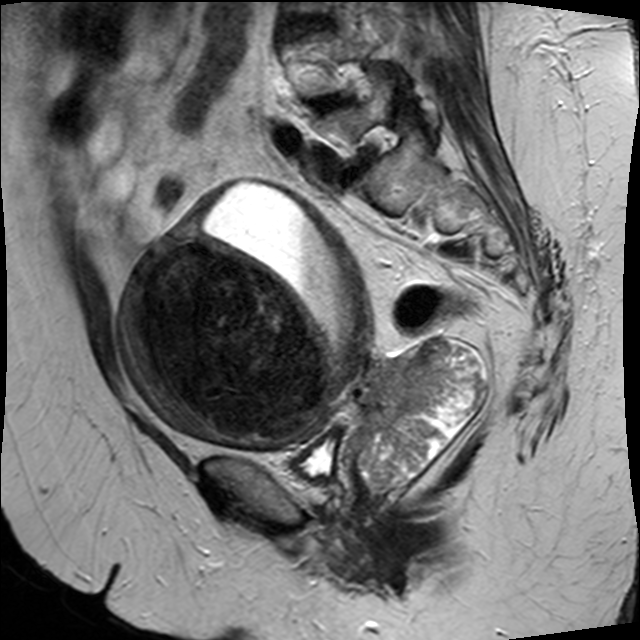
Pelvic MRI for cervical cancer, one sagittal slice; slice 14 of 34 in the series (ordered by position); T2-weighted; 1.5 T; TE 89 ms, TR 3320 ms; 640 × 640 image matrix, field of view 260 × 260 mm. Patient: female, 50 years.
Annotated regions visible in this slice (outlined manually by an expert reader):
- uterus and cervix: bounding box [x1, y1, x2, y2] px = [116, 180, 488, 493]